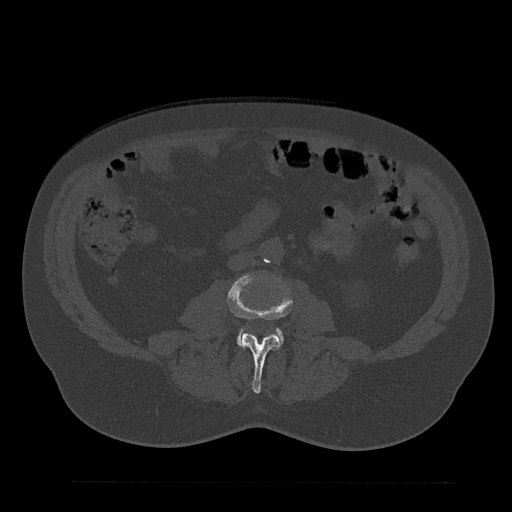
CT including the spine, one axial slice; position 11 of 797 along the scan axis; reconstruction kernel Br40s/3; 120 kVp; bone window (W 1800 / L 400 HU); 0.5 mm slice thickness; 512 × 512 image matrix, field of view 430 × 430 mm. Male patient, age 61 years. From the clinical record (not read from this slice): primary cancer: prostate.
Structures marked on this image (semi-automatically segmented with operator editing):
- L3 vertebra: bounding box (x1, y1, x2, y2) in pixels: (228, 273, 292, 393)
- L4 vertebra: (237, 329, 283, 345)